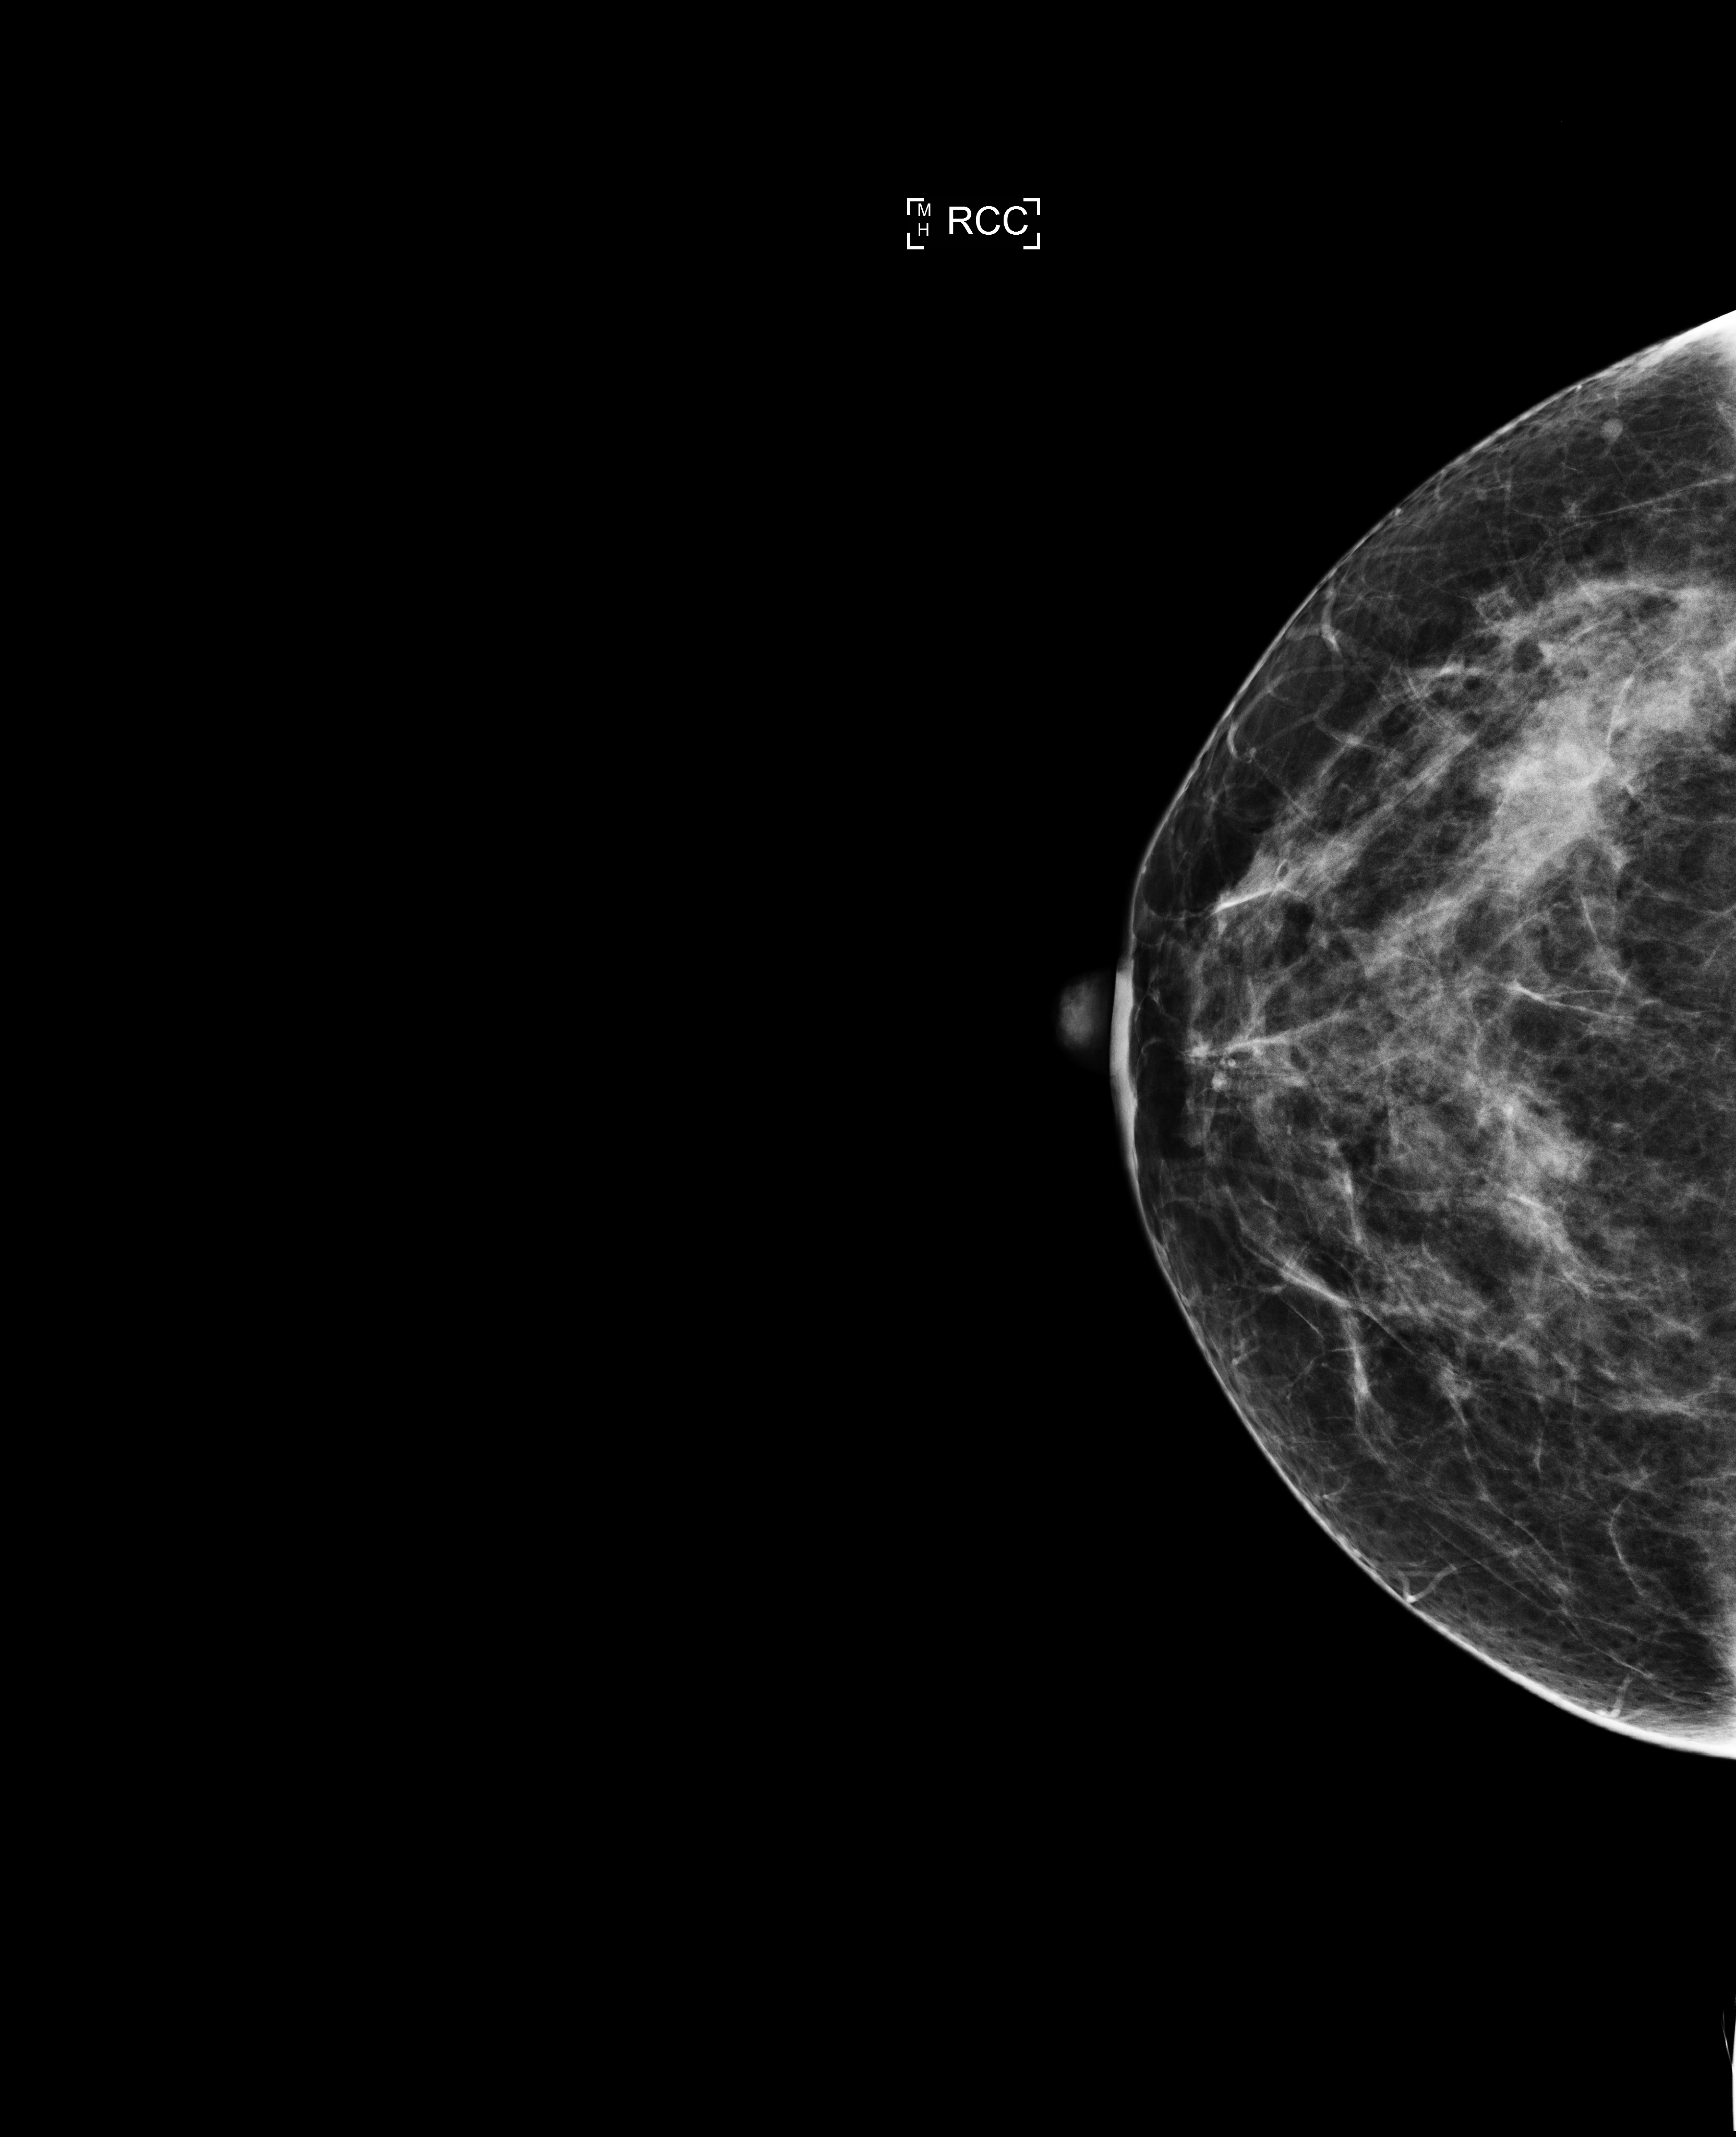
Full-field digital mammogram (FFDM), right breast, craniocaudal (CC) view, screening examination. Female patient, age 46 years.
BI-RADS breast density category at the screening exam (both breasts, scale 1–4): 3. Final BI-RADS category for the screening round (tomosynthesis exam, both breasts): category 1. Recall: no recall after this screen.